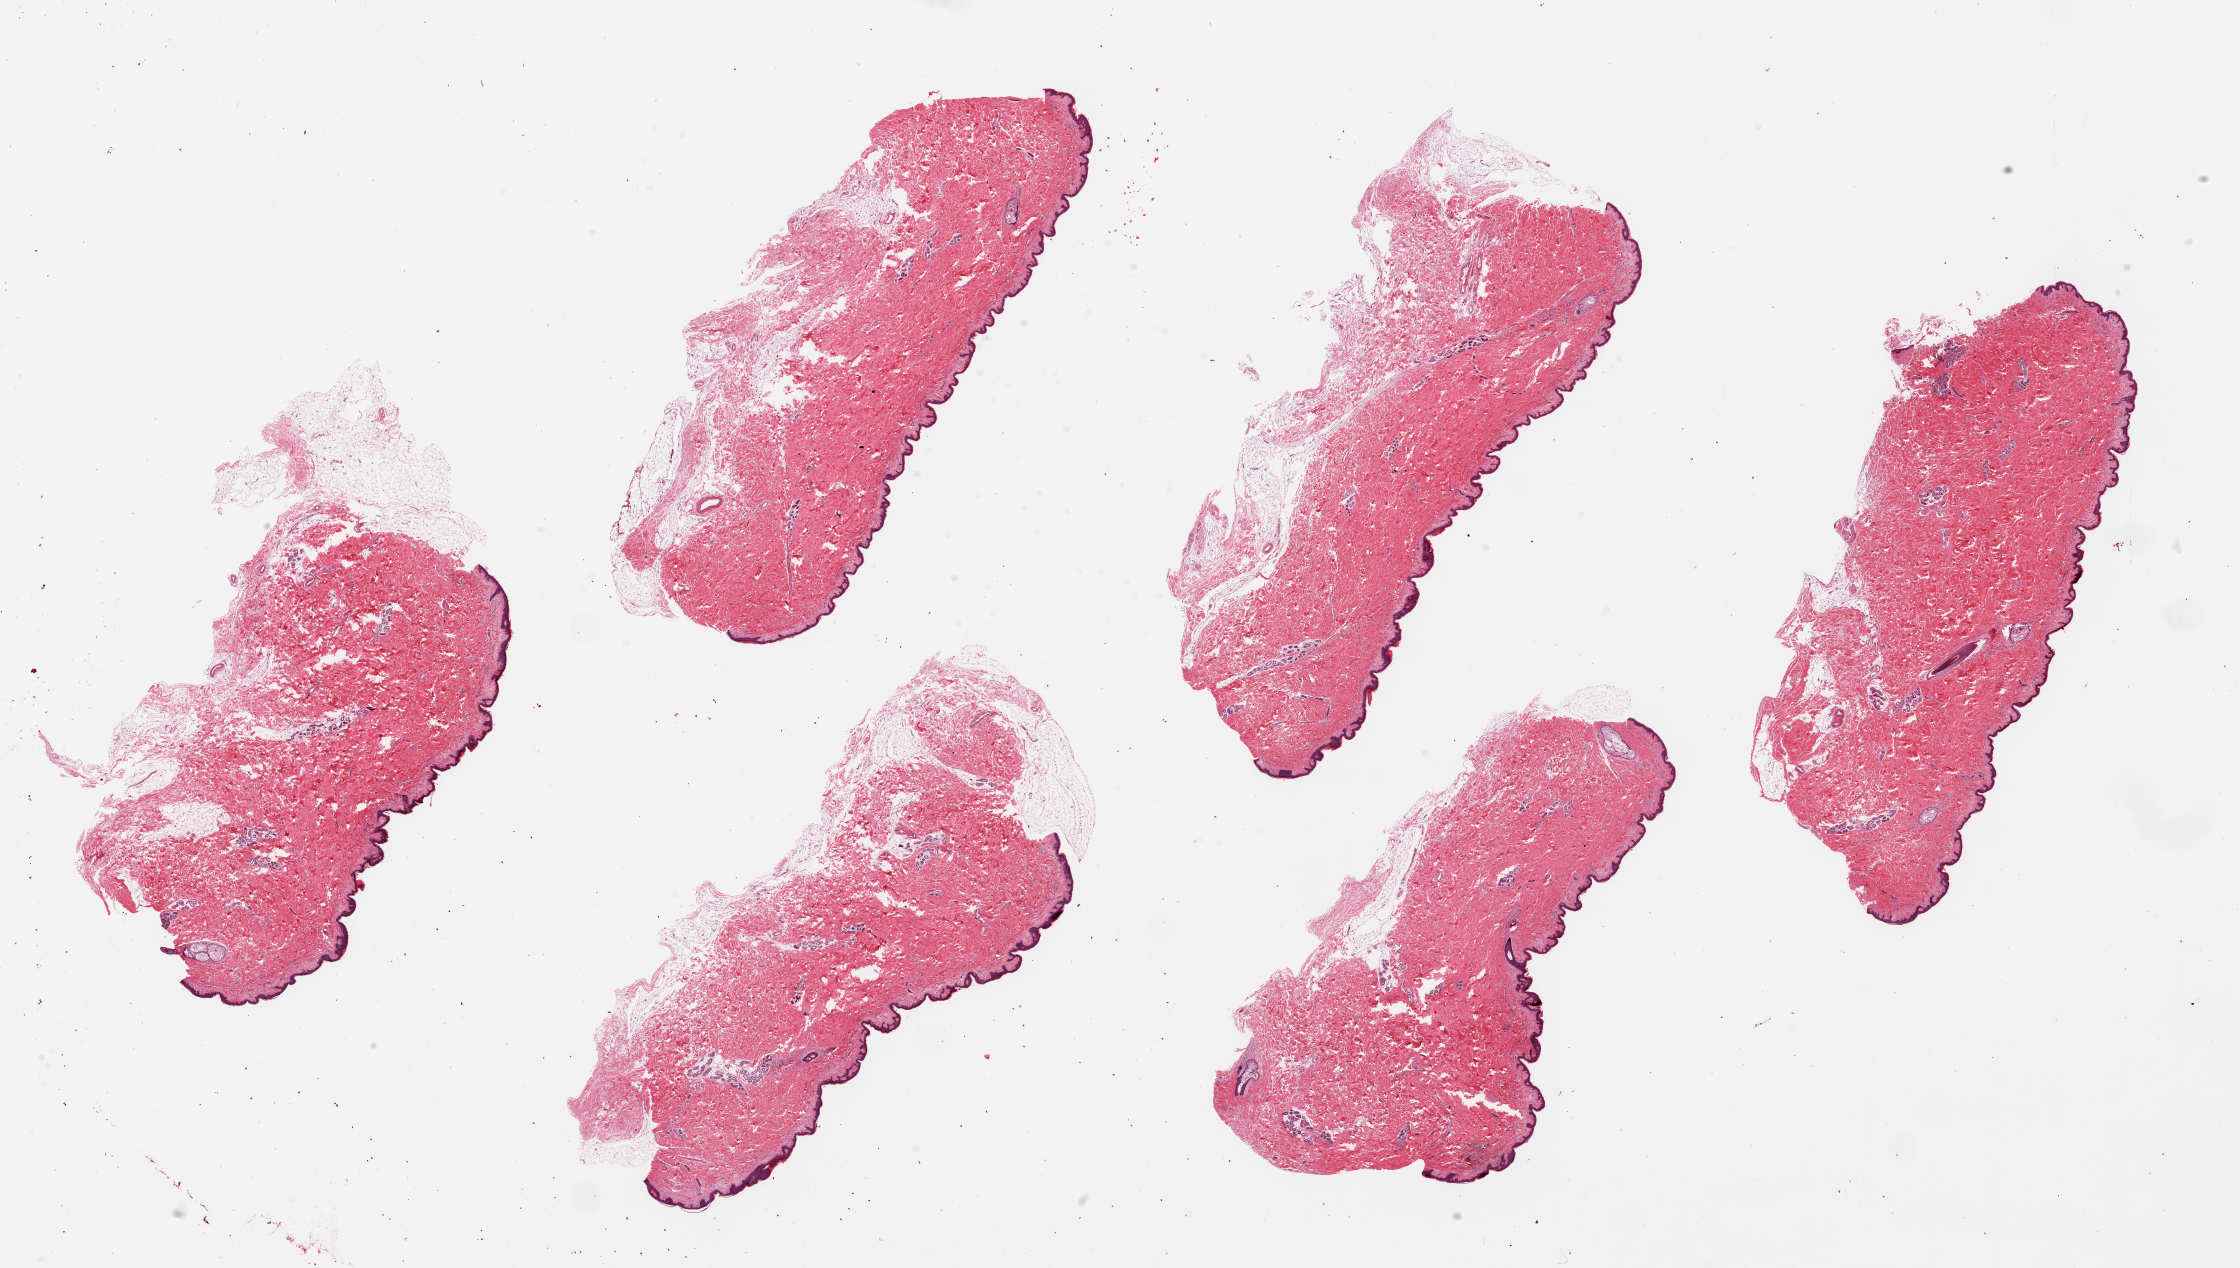
Whole-slide image, H&E stain, brightfield — a low-resolution overview of the entire scanned area, about 35.4 x 20.1 mm (acquisition: 20x scan). PAXgene-fixed paraffin-embedded (PFPE) section. Sampled site (target tissue): skin of suprapubic region. Tissue donor sample.
Reviewer comment on this tissue sample: 6 pieces ~10x3mm. Squamous epithelium is ~1-2% thickness.